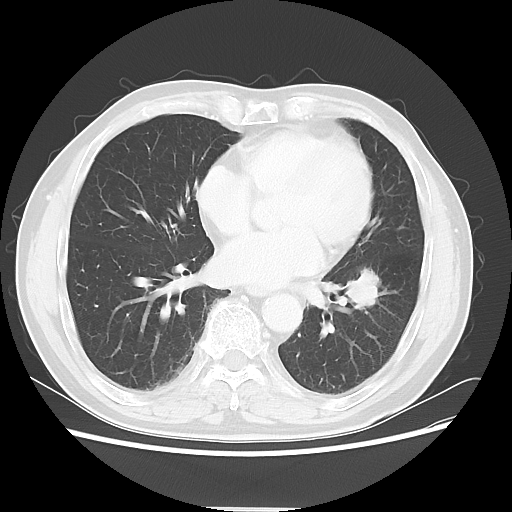
Chest CT, one axial slice; position 24 of 64 along the scan axis; reconstruction kernel LUNG; lung window (W 1500 / L -600 HU); 5 mm slice thickness; 512 × 512 image matrix, field of view 366 × 366 mm. Male patient, age 71 years. Case-level facts recorded for this patient, not image findings: clinical TNM (as recorded): T1c N1 M0; histopathological grade: G2-3.
Annotated regions visible in this slice (rectangle marked by the reading radiologist):
- lung tumour (recorded histology: adenocarcinoma): bounding box [x1, y1, x2, y2] px = [338, 259, 384, 321]